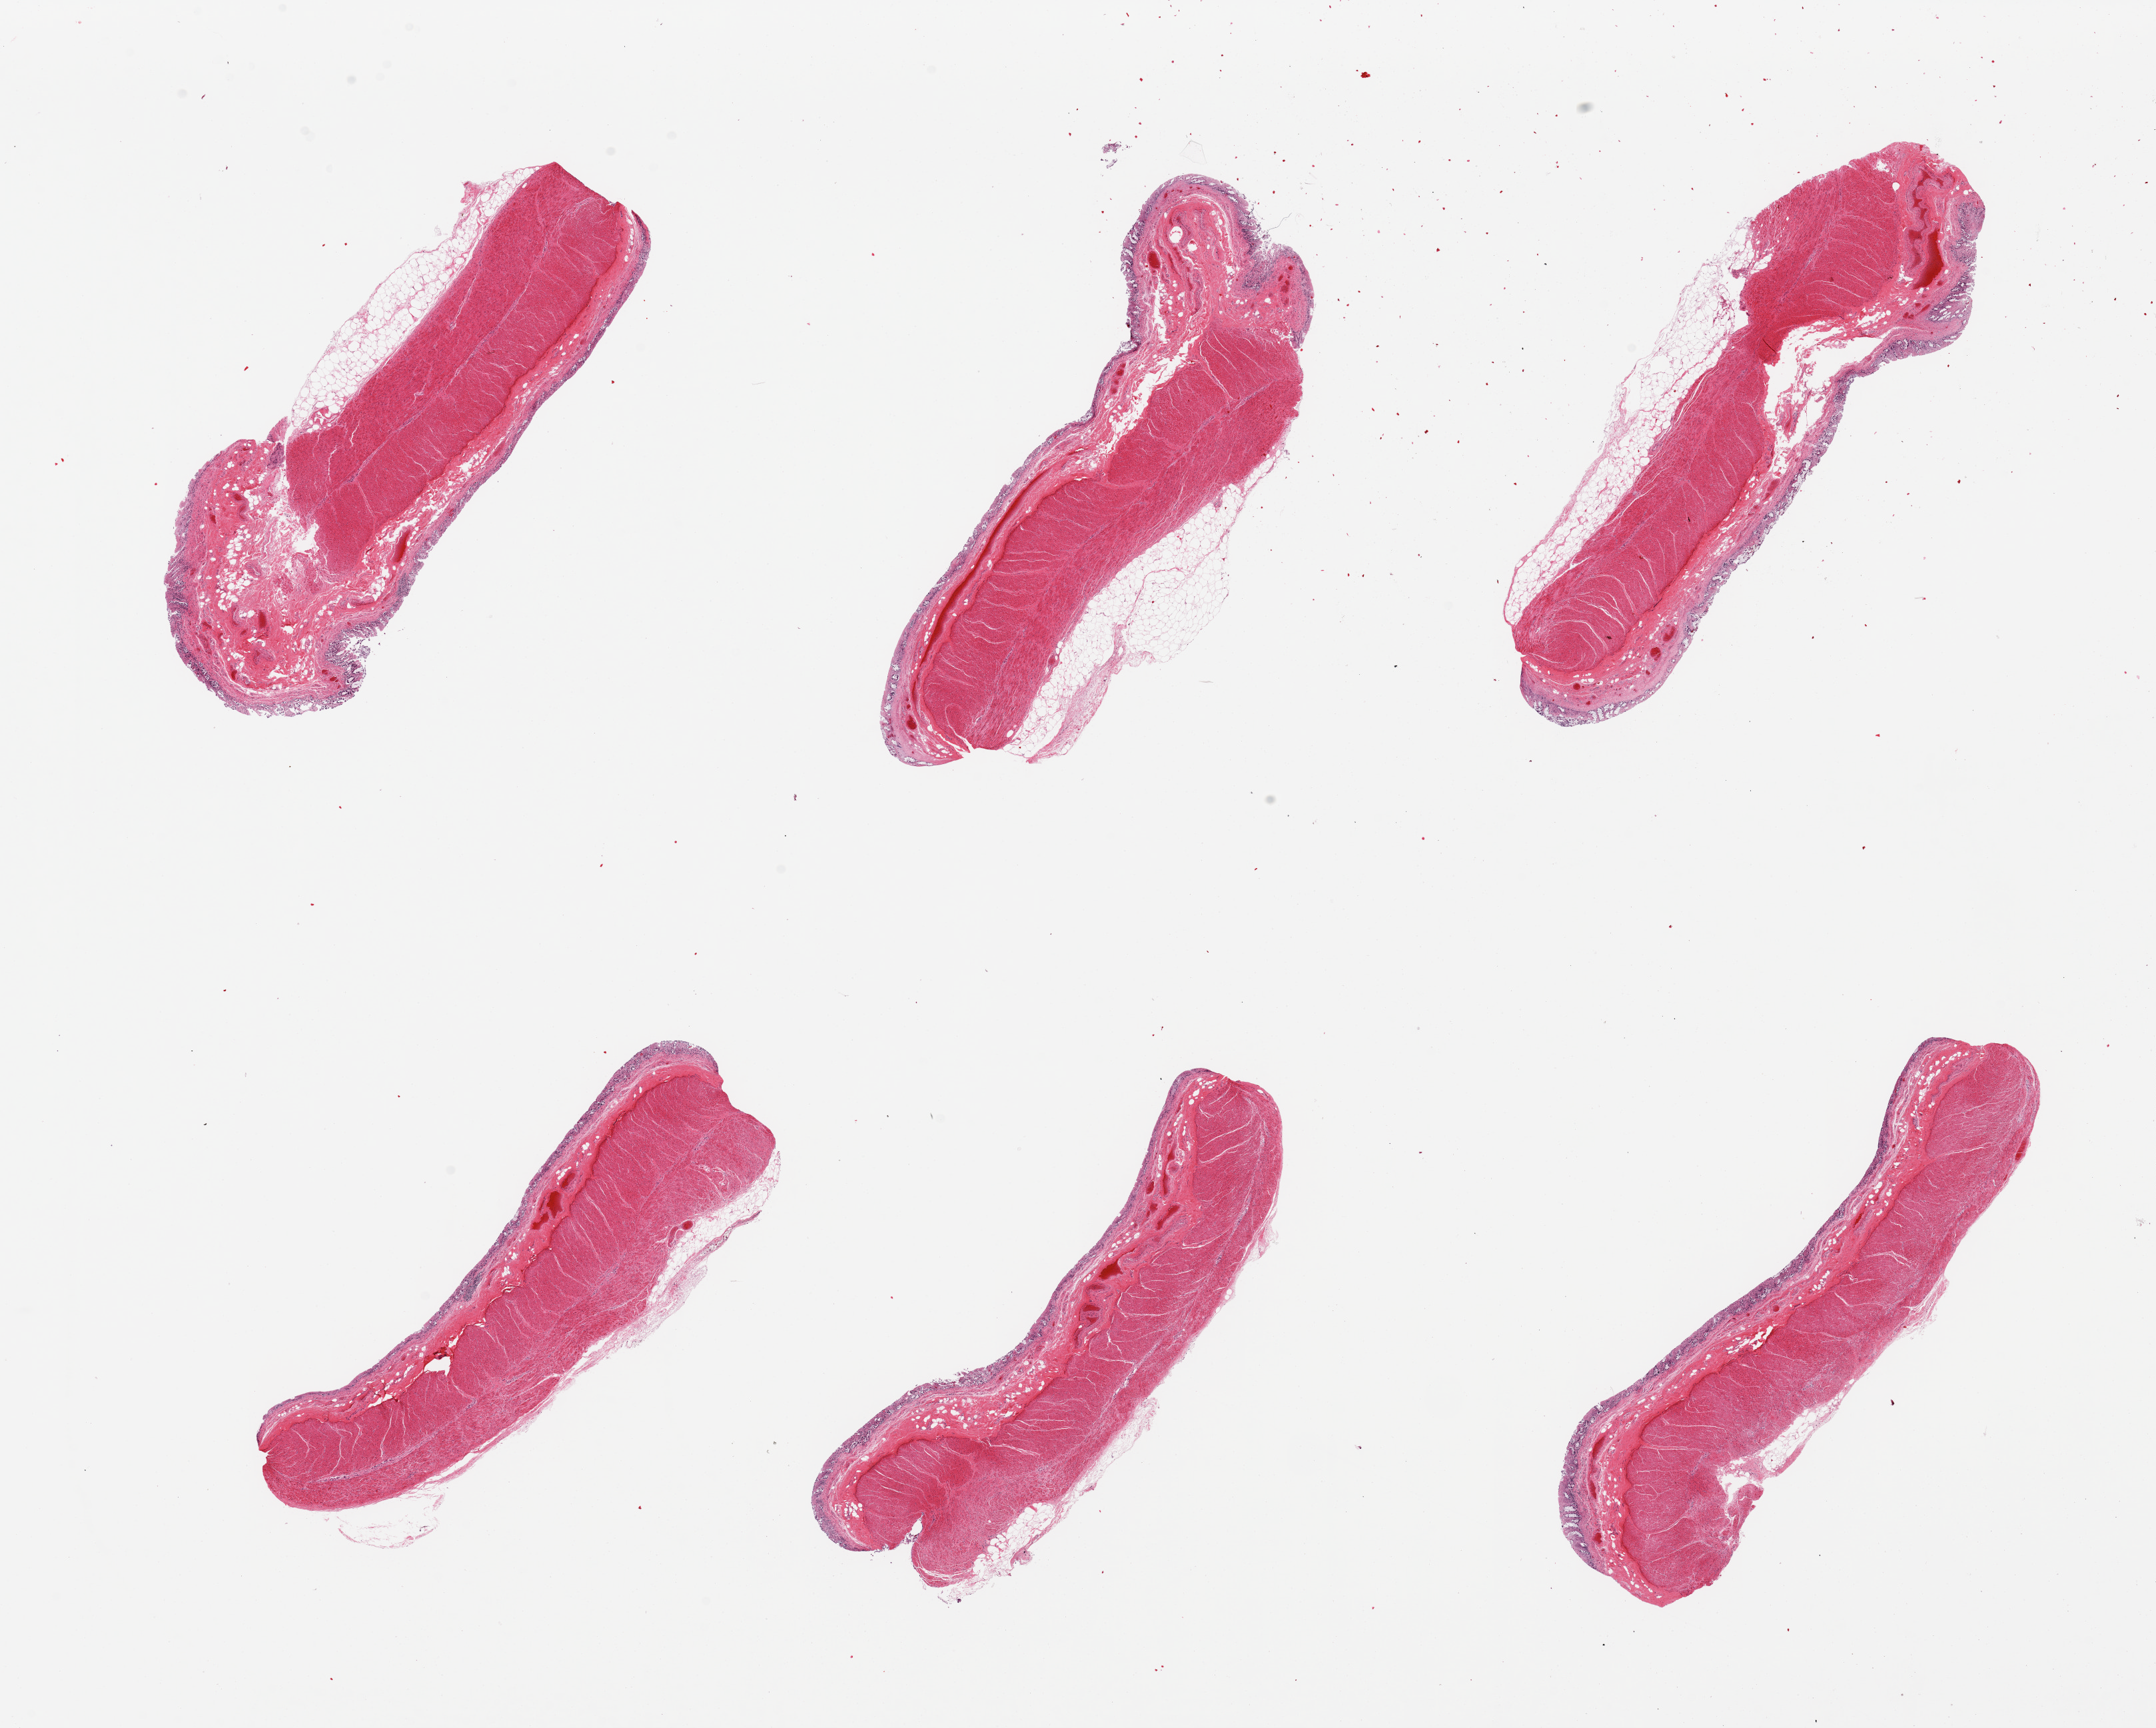
H&E whole-slide image, a low-resolution overview of the entire scanned area, about 25.6 x 20.5 mm. PAXgene-fixed, paraffin-embedded tissue. Sampled site (target tissue): transverse colon. Tissue donor sample. Donor: female.
Review note (as recorded): 6 pieces, mucosa severely autolyzed, muscle is better preserved.